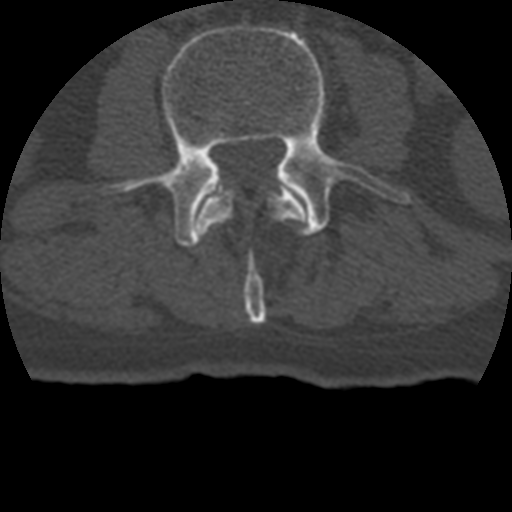
CT including the spine, one axial slice. Slice 98 of 399 in the series (ordered by position). 120 kVp. Bone window (W 1800 / L 400 HU). 1.25 mm slice thickness. 512 × 512 image matrix. Patient age 69 years. Case-level facts recorded for this patient, not image findings: primary cancer: prostate.
Structures marked on this image (semi-automatic segmentation, software-assisted and operator-edited):
- L2 vertebra: bounding box [x1, y1, x2, y2] px = [197, 187, 306, 324]
- L3 vertebra: [103, 25, 410, 246]